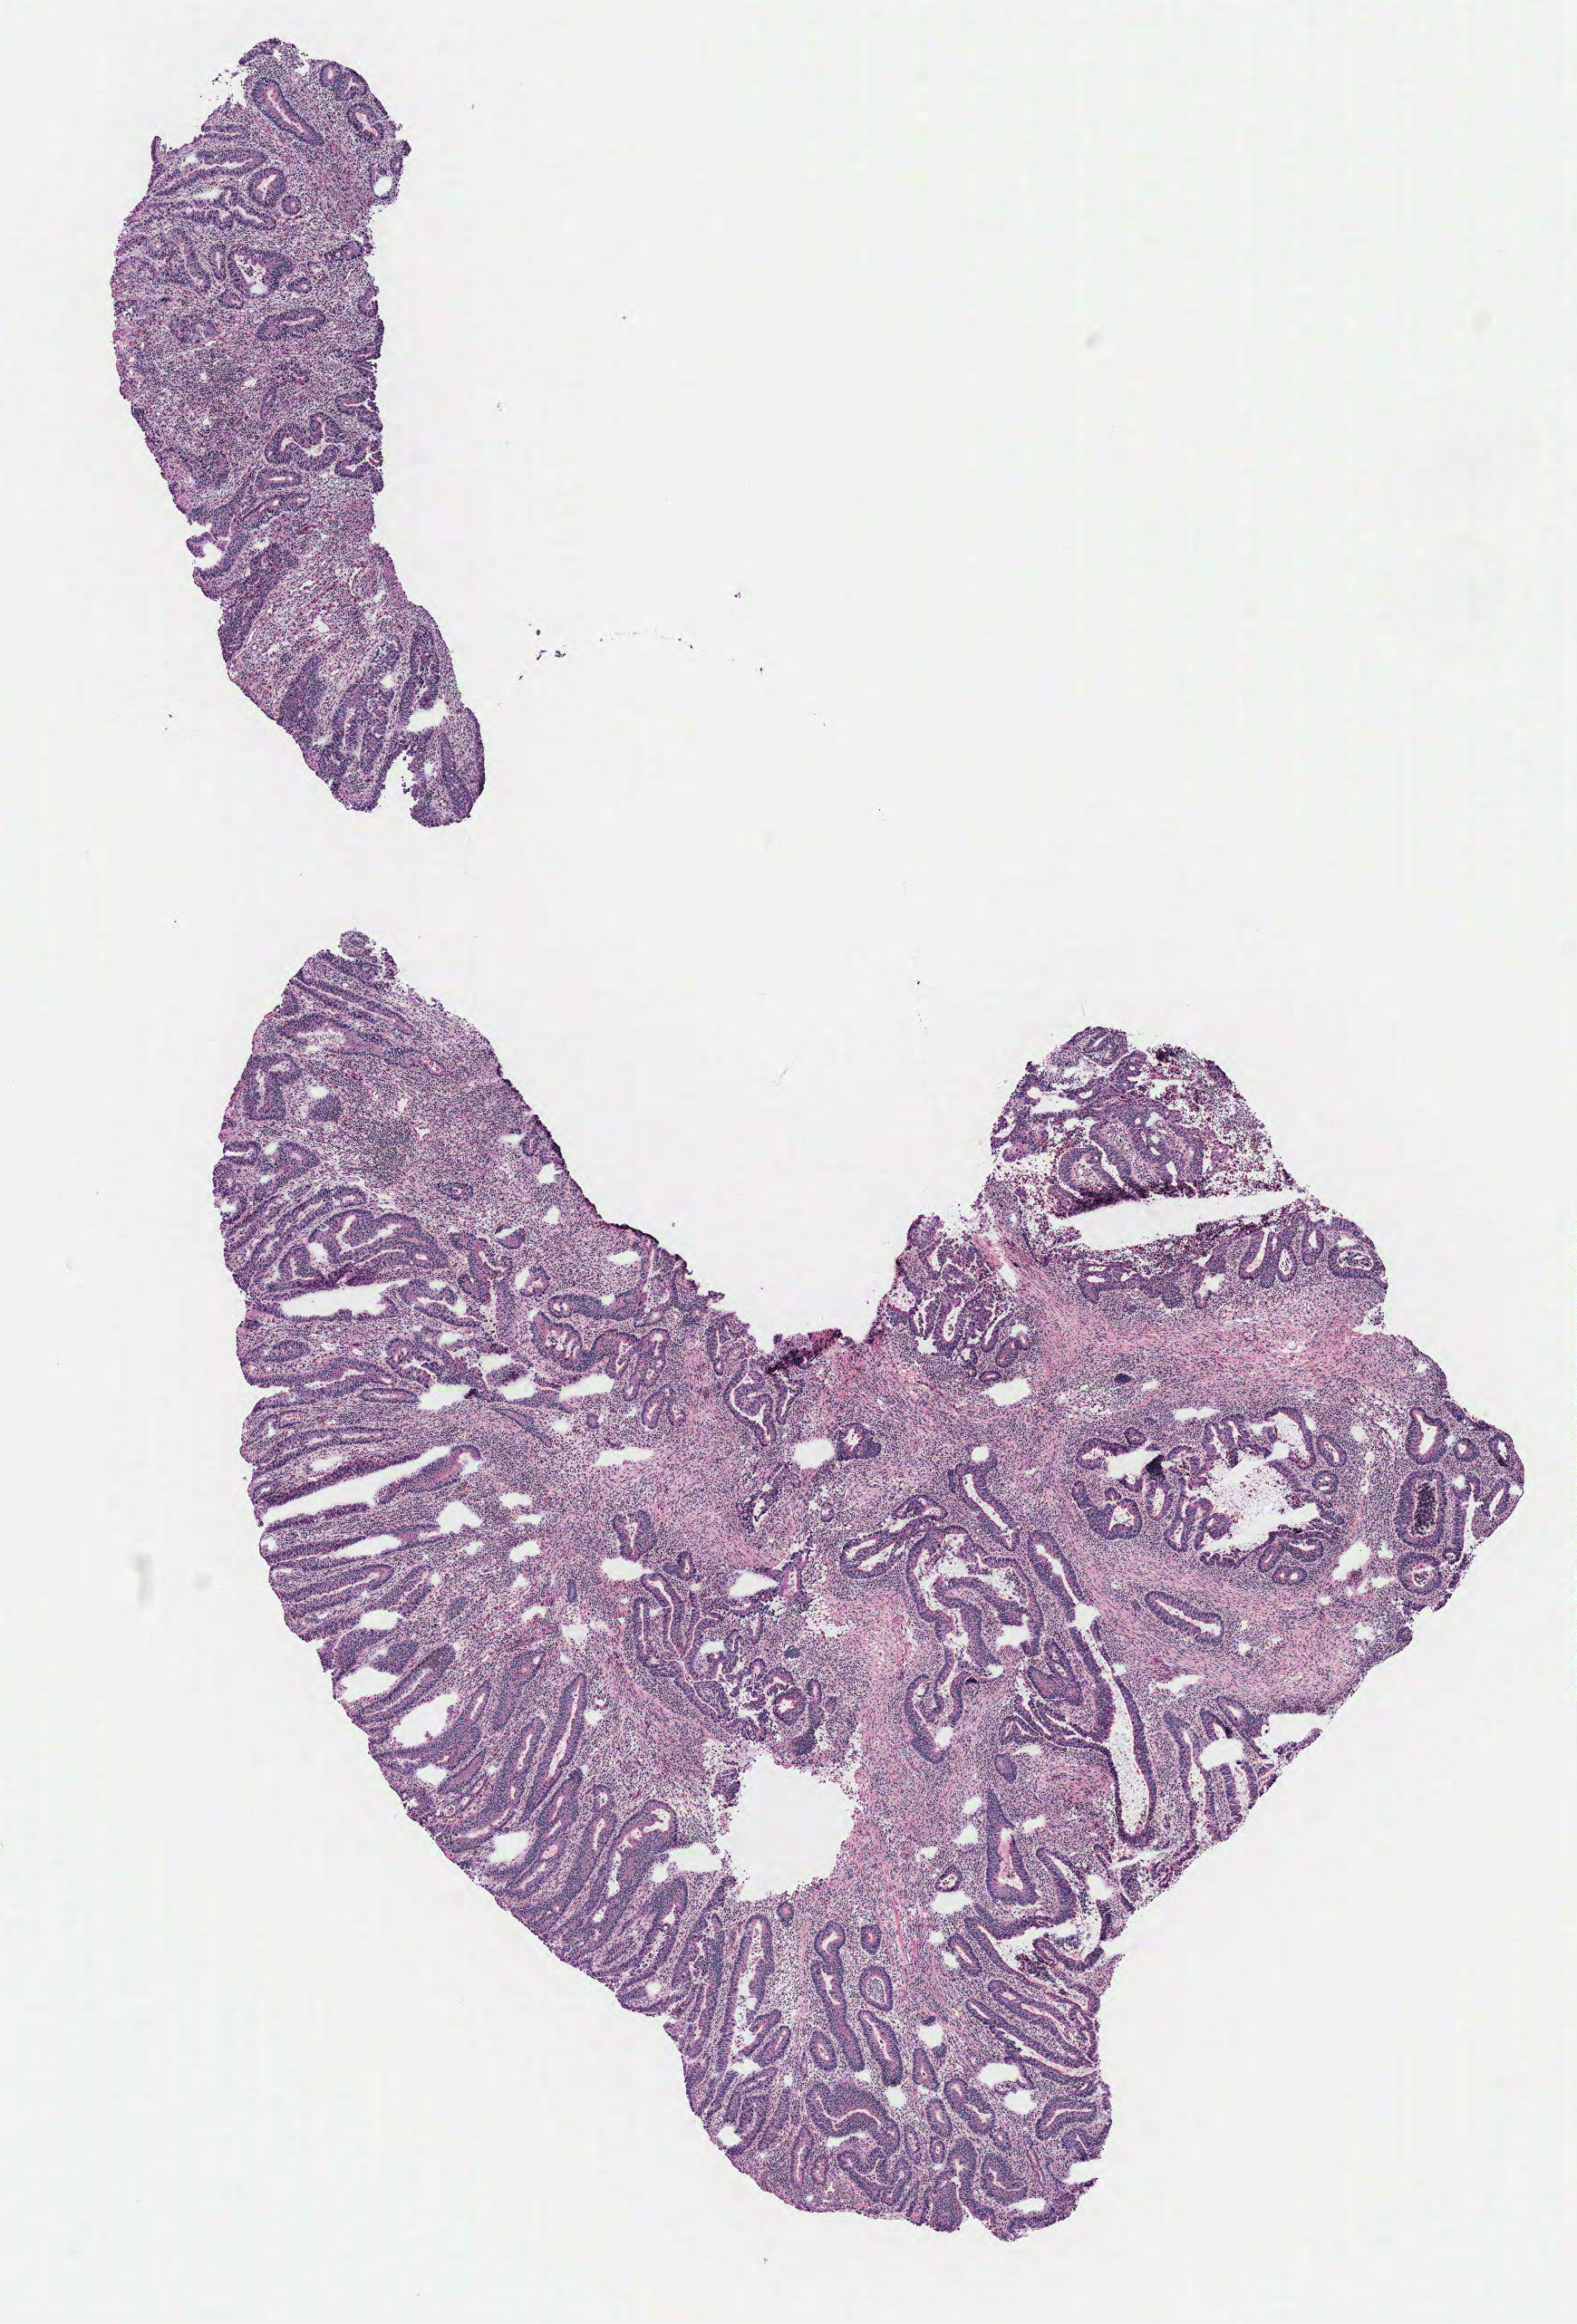
H&E whole-slide image, low-resolution overview of the scanned area, about 7.0 x 10.3 mm; colon, tissue type not recorded.
Patient diagnosis (cohort enrolment): colon cancer (colon).